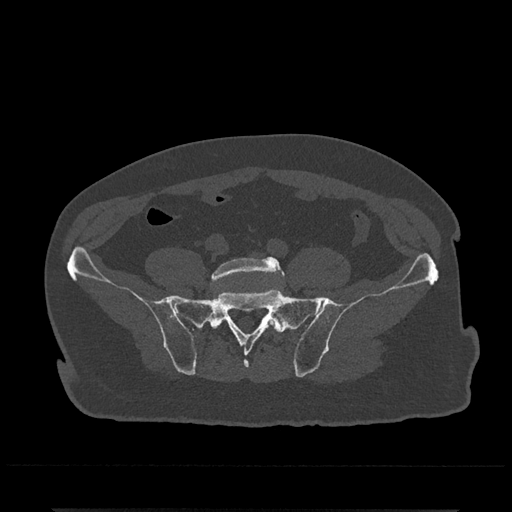
CT including the spine, one axial slice; slice 43 of 797 in the series (ordered by position); reconstruction kernel Br40s/3; 120 kVp; bone window (W 1800 / L 400 HU); 0.5 mm slice thickness; 512 × 512 image matrix. Male patient, age 67 years. Case-level facts recorded for this patient, not image findings: primary cancer: prostate.
Structures marked on this image (semi-automatic segmentation, software-assisted and operator-edited):
- L5 vertebra: bounding box <210,257,285,328> (left, top, right, bottom; pixels)